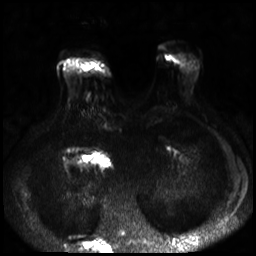
Breast MRI, one axial slice. Slice 7 of 30 in the series (ordered by position). Diffusion-weighted series; image 2 of 4 stored at this slice position (different b-values; order by instance number). 3 T. 4 mm slice thickness. 256 × 256 image matrix, field of view 320 × 320 mm. Female patient.
Outlined on this slice (outlined manually by an expert reader):
- tumour on diffusion-weighted imaging: bounding box <98,68,104,75> (left, top, right, bottom; pixels)